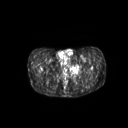
FDG PET of an extremity soft-tissue mass (from a PET/CT study), one axial slice. Position 43 of 267 along the scan axis. 128 × 128 image matrix, field of view 600 × 600 mm. Male patient, age 59 years. From the clinical record (not read from this slice): histological type: pleiomorphic liposarcoma; grade: high; site of the primary tumour: left thigh.
Structures marked on this image (expert contour drawn on MRI and transferred to this co-registered scan by the dataset authors):
- gross tumour volume including surrounding oedema: bounding box [x1, y1, x2, y2] px = [70, 64, 83, 77]
- gross tumour volume (mass): [72, 65, 81, 72]